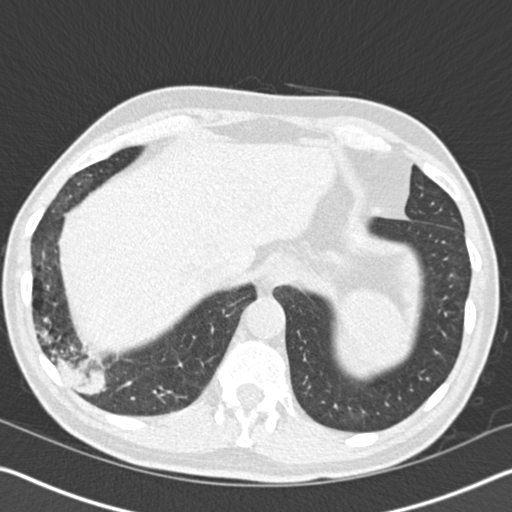
Axial slice from a low-dose chest CT screening exam; baseline screening round; lung window (W 1500 / L -600 HU); 2 mm slice thickness; standard (soft-tissue) reconstruction kernel (B30f); slice 127 of 161 in the series; 512 × 512 image matrix, field of view 340 × 340 mm. Male, age 61 years at enrolment. Current smoker at enrolment.
Expert reader's lesion annotation, bounding box (x1, y1, x2, y2) in pixels: (7, 270, 135, 413). Screening reader's record for this exam (one nodule recorded; not confirmed to be the boxed lesion): non-calcified nodule or mass ≥4 mm, right lower lobe, 52 × 36 mm, spiculated (stellate) margins, soft tissue attenuation. Official screen result: positive, change unspecified: nodule(s) >= 4 mm or enlarging nodule(s), mass(es), or other non-specific abnormalities suspicious for lung cancer. Later outcome: lung cancer diagnosed 392 days after this screen — bronchiolo-alveolar adenocarcinoma, NOS, right lower lobe, moderately differentiated (G2), stage IIIB (AJCC 6th edition), 90 mm at pathology.